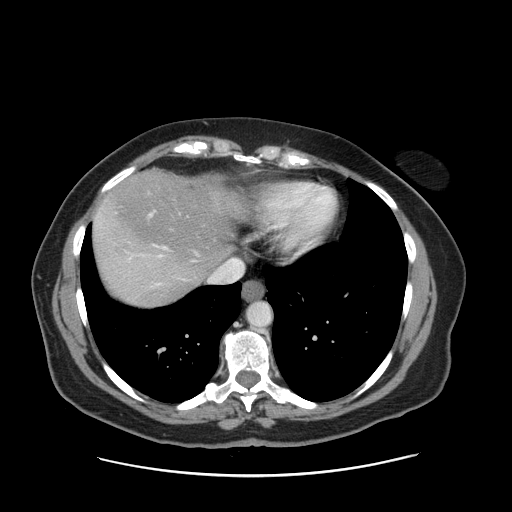
Contrast-enhanced abdominal CT, one axial slice; slice 137 of 161 in the series (ordered by position); 120 kVp; intravenous contrast given; soft-tissue window (W 400 / L 40 HU); 512 × 512 image matrix. Female patient, age 62 years. From the clinical record (not read from this slice): diagnosis: colorectal cancer liver metastases, imaged before liver resection; multiple liver metastases: no.
Outlined on this slice (manually delineated by an expert):
- hepatic veins: bounding box (x1, y1, x2, y2) in pixels: (128, 190, 243, 286)
- liver: (94, 172, 241, 306)
- planned liver remnant (the part of the liver to remain after resection): (97, 172, 239, 275)
- portal vein (with intrahepatic branches): (150, 213, 153, 216)